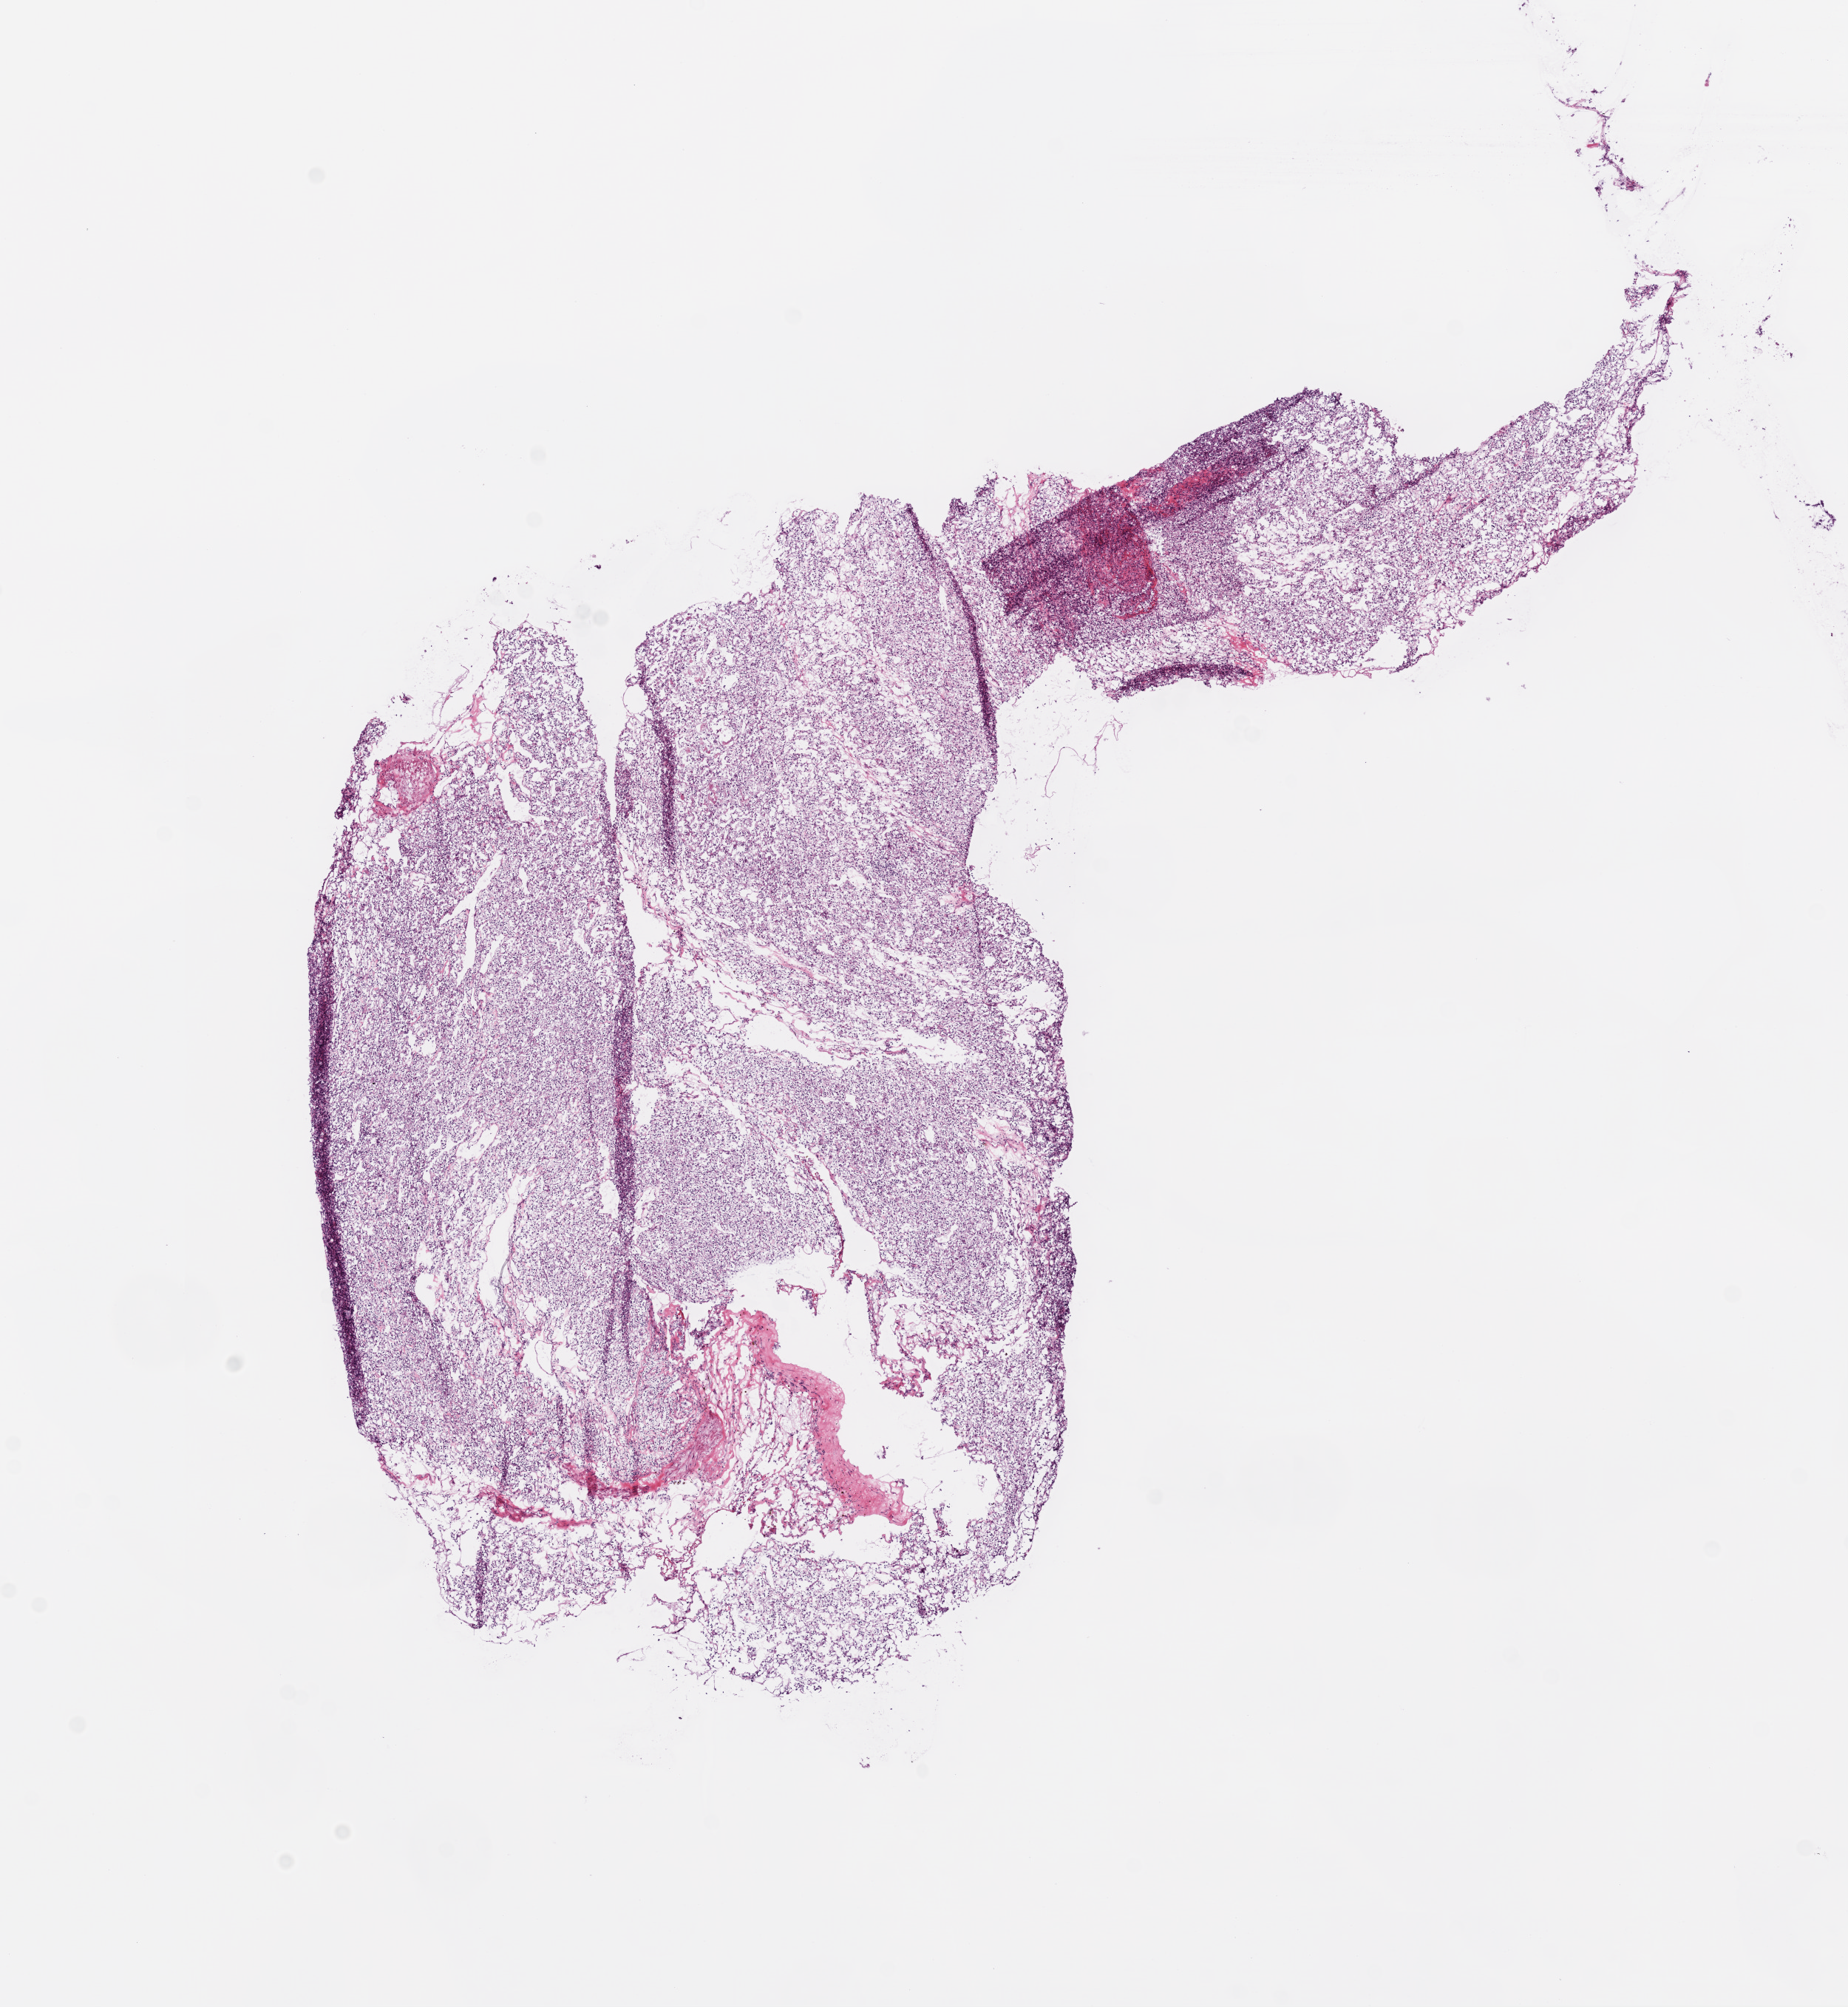
Hematoxylin and eosin (H&E) stained whole-slide image, a low-resolution overview of the entire scanned area, about 10.0 x 10.9 mm (acquisition: 20x scan), frozen section, sample: primary tumour, kidney. Patient: female, age at initial diagnosis 60 years. Histologic grade: G2 (moderately differentiated). Pathologist review of this section (percent, as recorded): tumour cells 85%, tumour nuclei 80%, normal cells 10%, stromal cells 5%, necrosis 0%.
AJCC pathologic stage: I. TNM: T1a N0 M0. Laterality: left. Diagnosis: Clear cell adenocarcinoma, NOS.